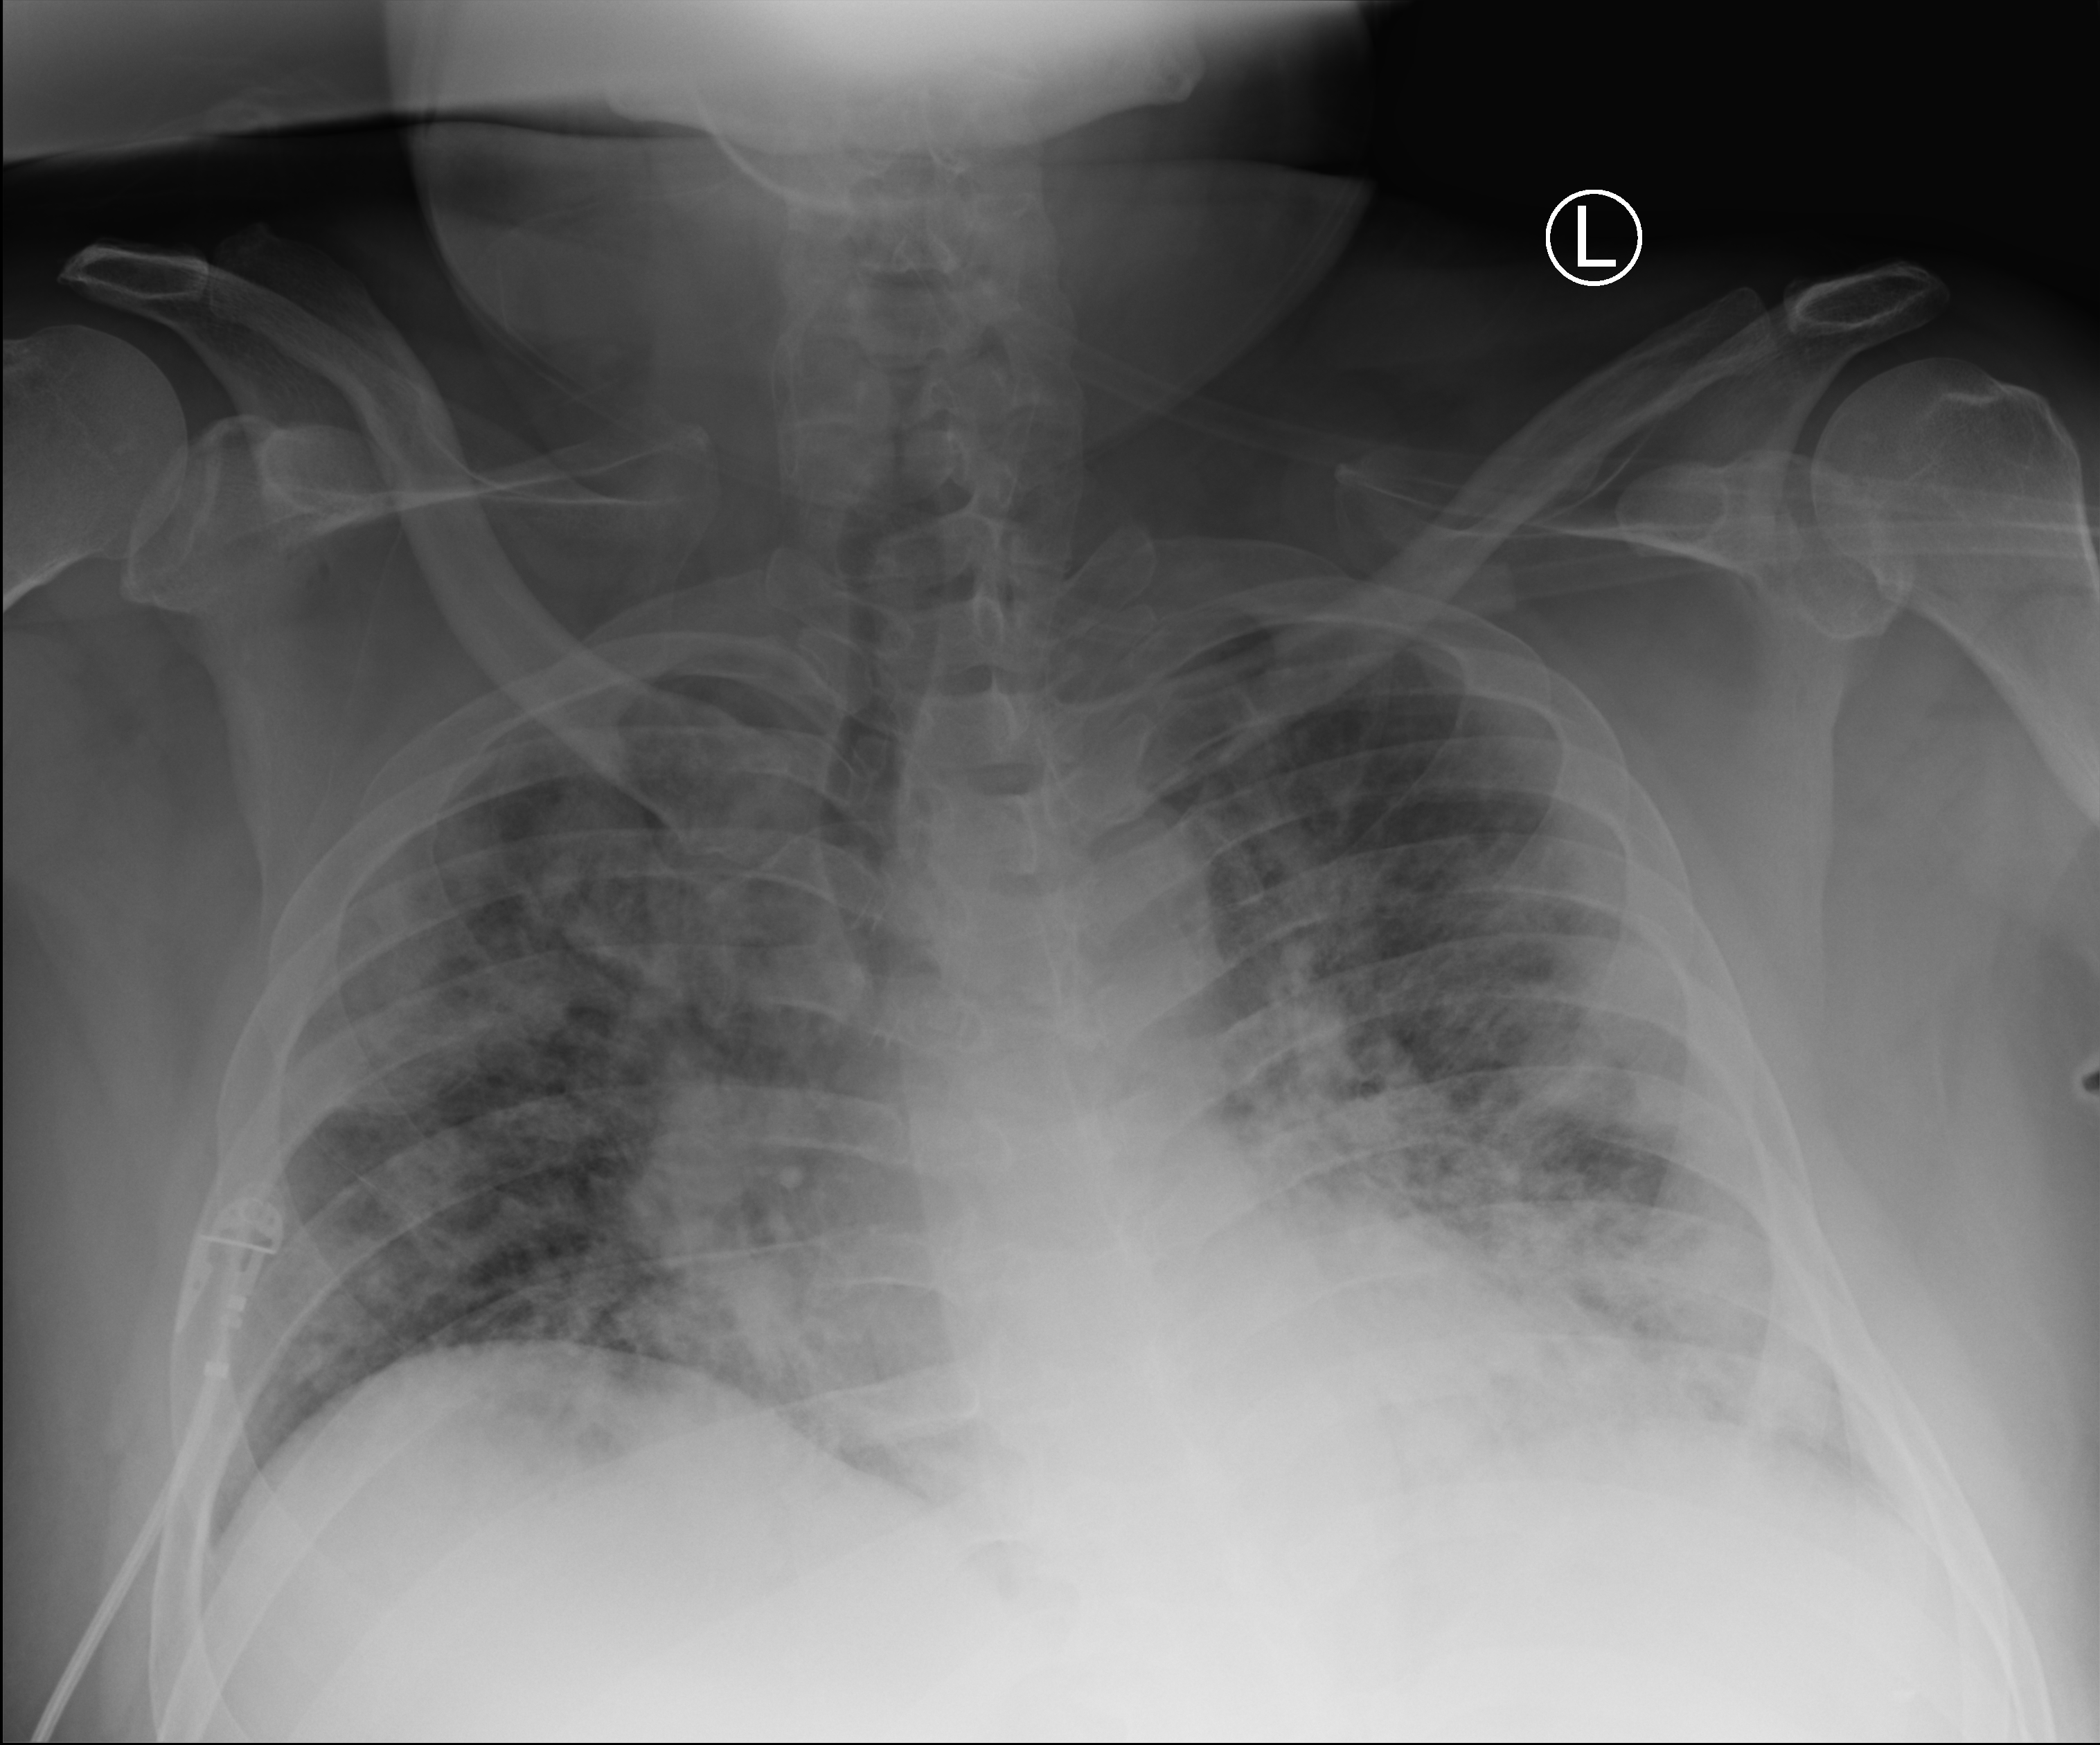
Portable chest radiograph; anteroposterior (AP) projection. Patient hospitalised with COVID-19; male, aged 18–59 years.
Admission-level facts for this patient (not findings on this image; timing relative to this image not recorded):
- length of hospital stay: 22 days
- admitted to intensive care during this hospital stay: no
- mechanically ventilated during this hospital stay: no